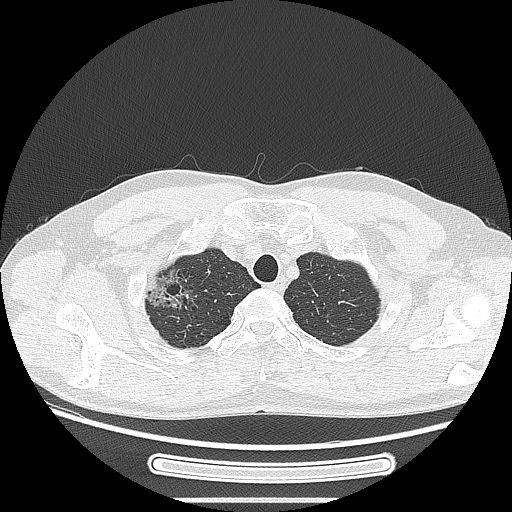
Chest CT, one axial slice; slice 231 of 269 in the series (ordered by position); reconstruction kernel LUNG; lung window (W 1500 / L -600 HU); 1.25 mm slice thickness; 512 × 512 image matrix. Male patient, age 53 years. From the clinical record (not read from this slice): clinical TNM (as recorded): T1c N0 M0; histopathological grade: G2.
Annotated regions visible in this slice (rectangle marked by the reading radiologist):
- lung tumour (recorded histology: adenocarcinoma): bounding box <137,256,200,317> (left, top, right, bottom; pixels)